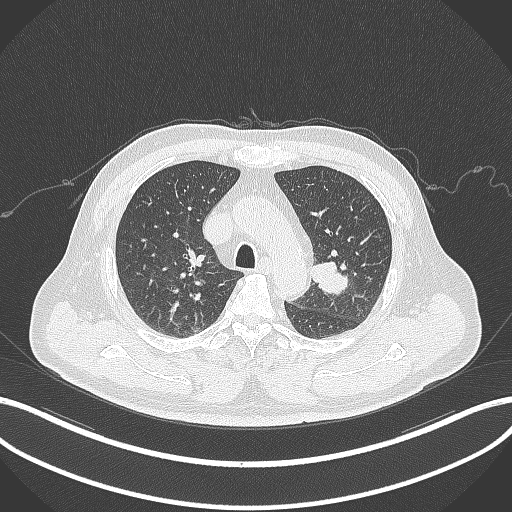
Chest CT, one axial slice. Reconstruction kernel B70f. 120 kVp. Lung window (W 1500 / L -600 HU). 1 mm slice thickness. 512 × 512 image matrix. Male patient, age 67 years. From the clinical record (not read from this slice): clinical TNM (as recorded): T2a N1 M0.
Structures marked on this image (rectangle marked by the reading radiologist):
- lung tumour (recorded histology: adenocarcinoma): bounding box <309,260,350,298> (left, top, right, bottom; pixels)